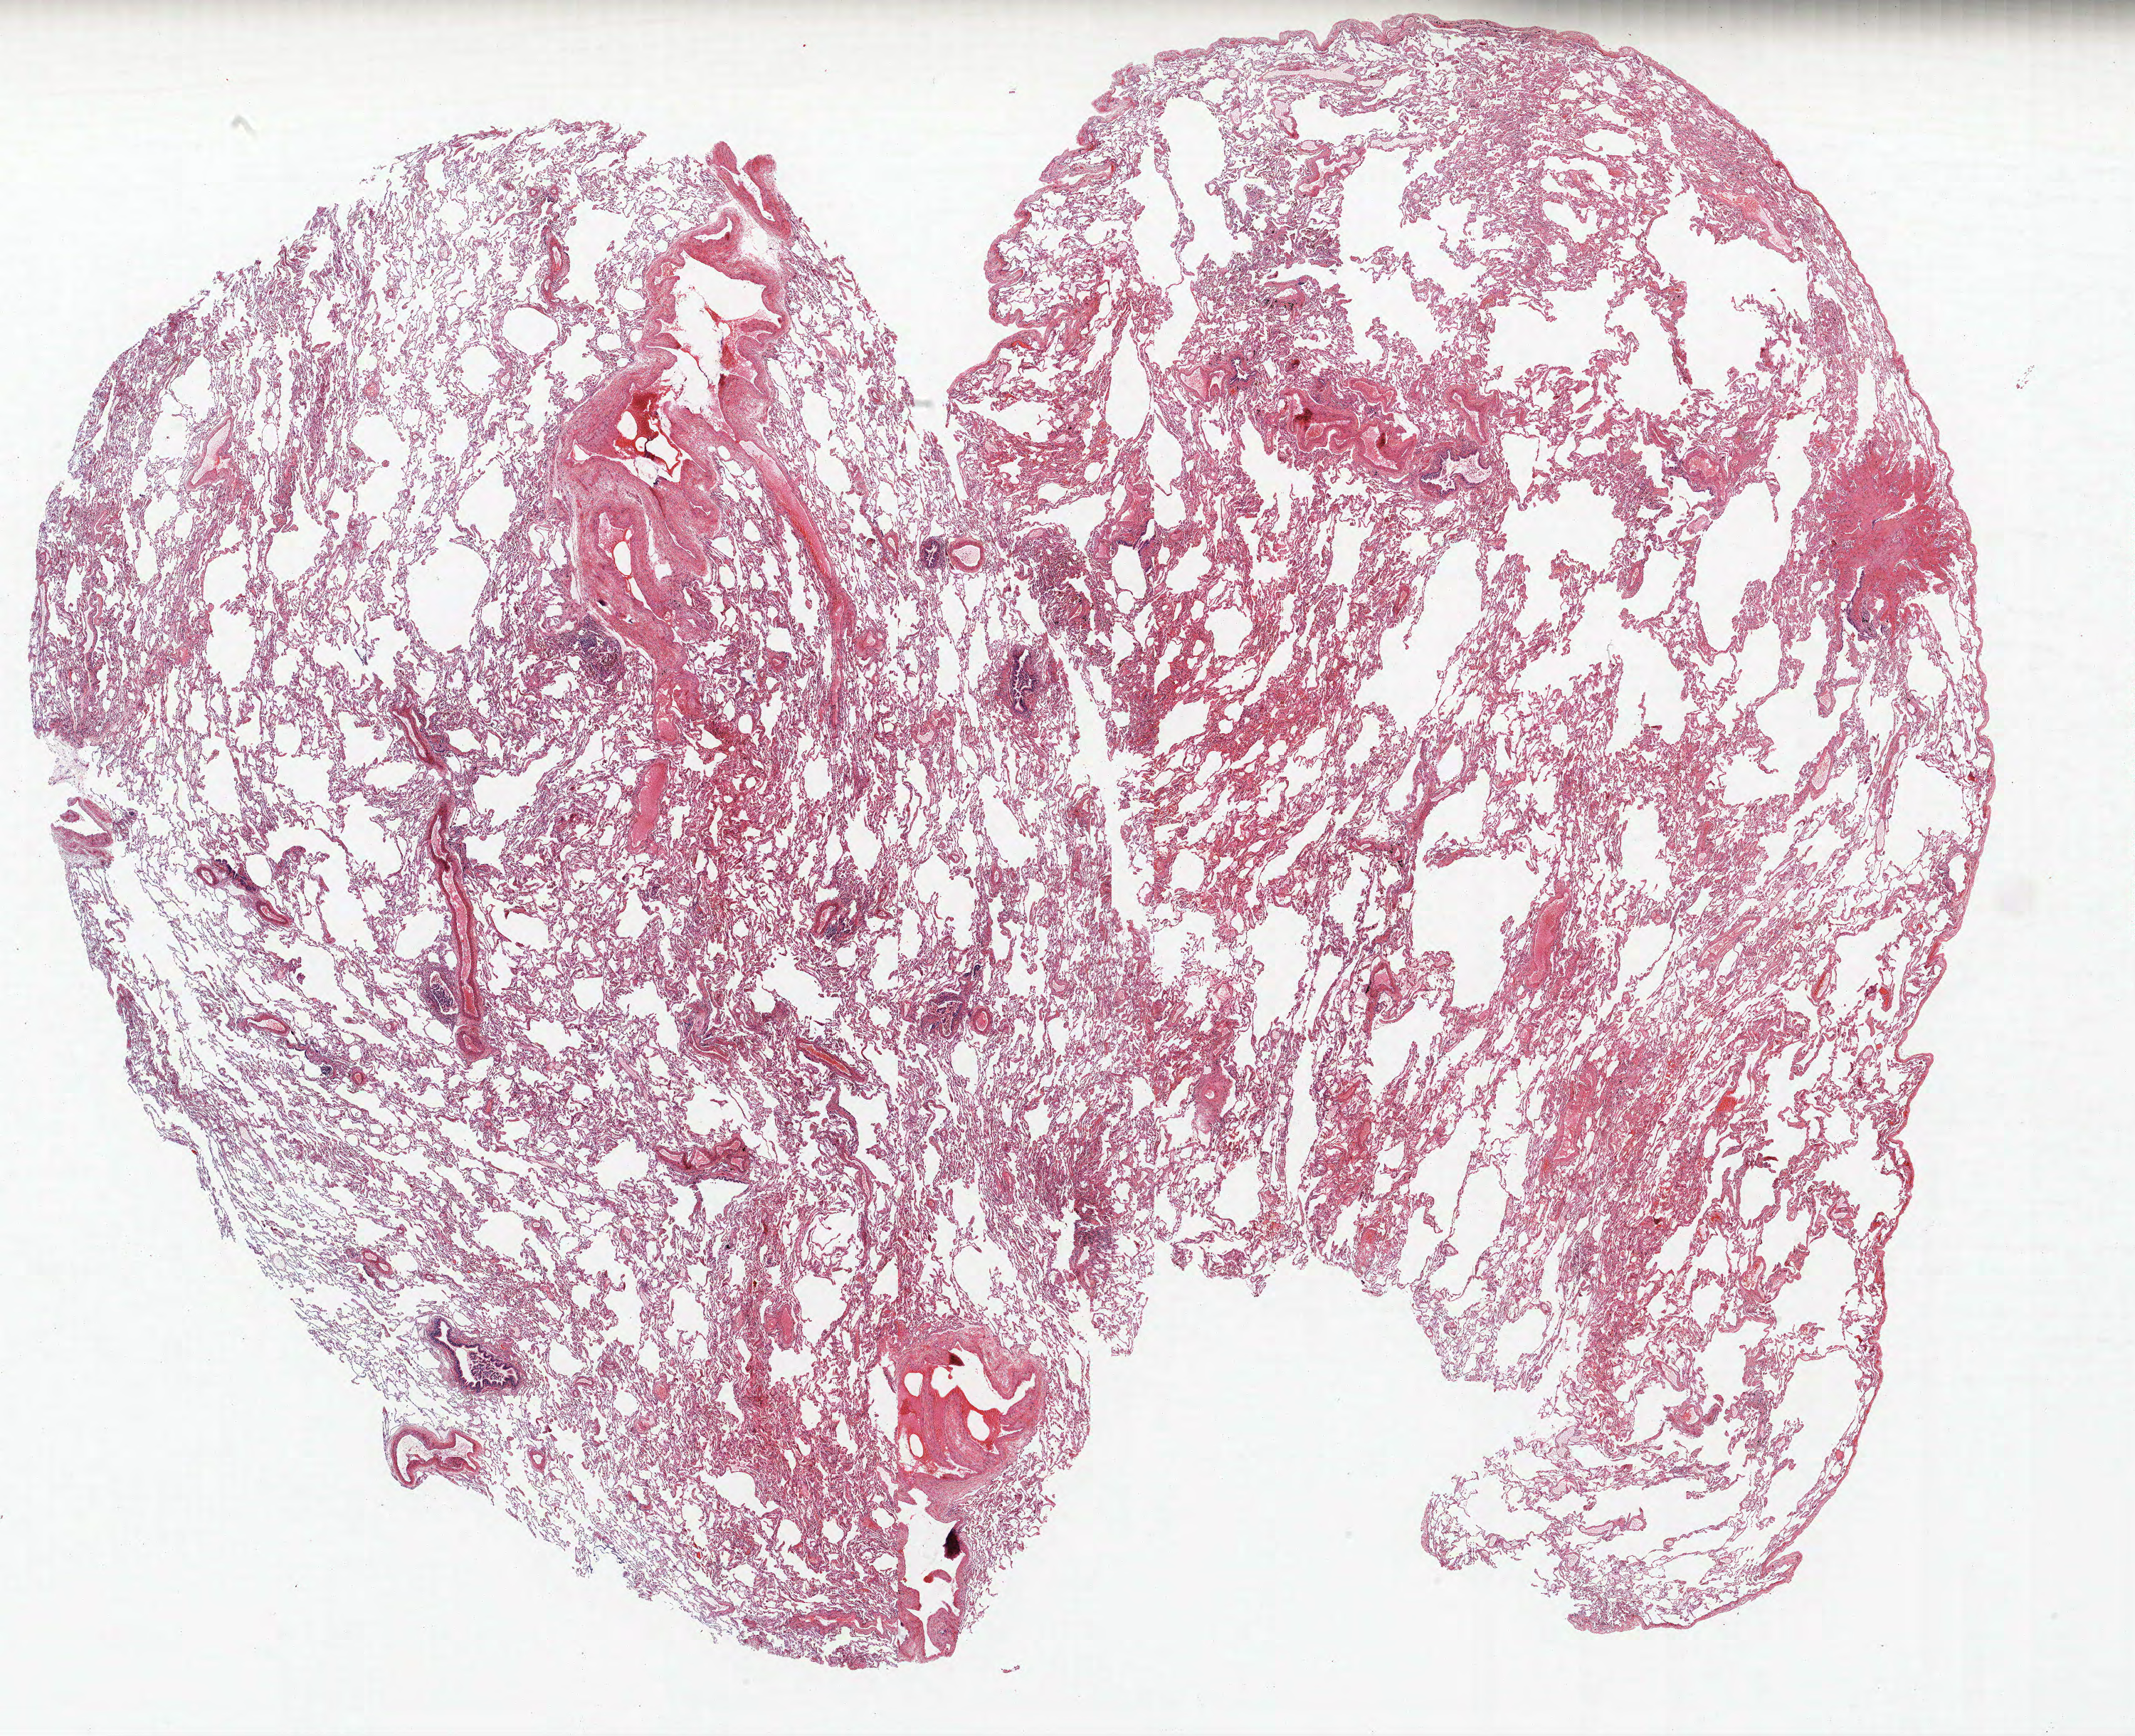
Hematoxylin and eosin (H&E) stained whole-slide image — low-resolution overview of the scanned area, about 24.0 x 19.5 mm; FFPE section; lung. Female patient, aged 68 at enrolment. Grade: moderately differentiated (G2).
Stage (AJCC 6th edition): IB. Tumour size (pathology): 40 mm. Primary tumour location (clinical record): left lower lobe. Participant's lung-cancer diagnosis: Adenocarcinoma, NOS (ICD-O-3 8140/3).